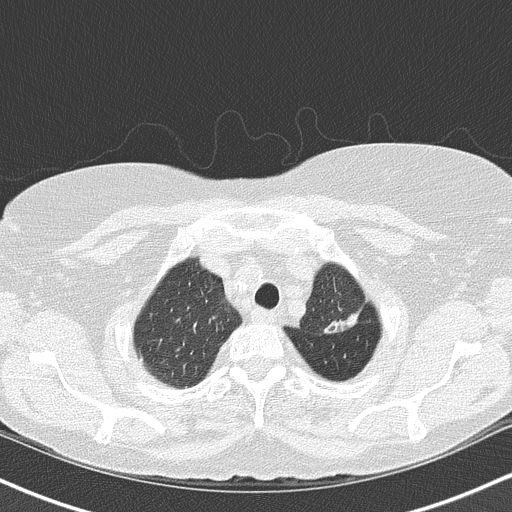
Low-dose screening chest CT, axial slice. Third screening round (two years after baseline). Lung window (W 1500 / L -600 HU). 2 mm slice thickness. Lung (sharp) reconstruction kernel (B50f). Slice 129 of 147 in the series. Female participant, aged 68 years at enrolment. Former smoker at enrolment.
Expert reader's lesion annotation, bounding box (x1, y1, x2, y2) in pixels: (285, 242, 378, 349). Reader record for this screening exam (exam-level; its link to the box is not recorded): non-calcified nodule or mass ≥4 mm, left upper lobe, 5 × 5 mm, poorly defined margins, mixed attenuation, pre-existing on the prior screen: yes; interval growth: yes. Lung cancer was diagnosed 42 days after this screen: adenocarcinoma, NOS, left upper lobe, poorly differentiated (G3), stage IB (AJCC 6th edition), 50 mm at pathology.